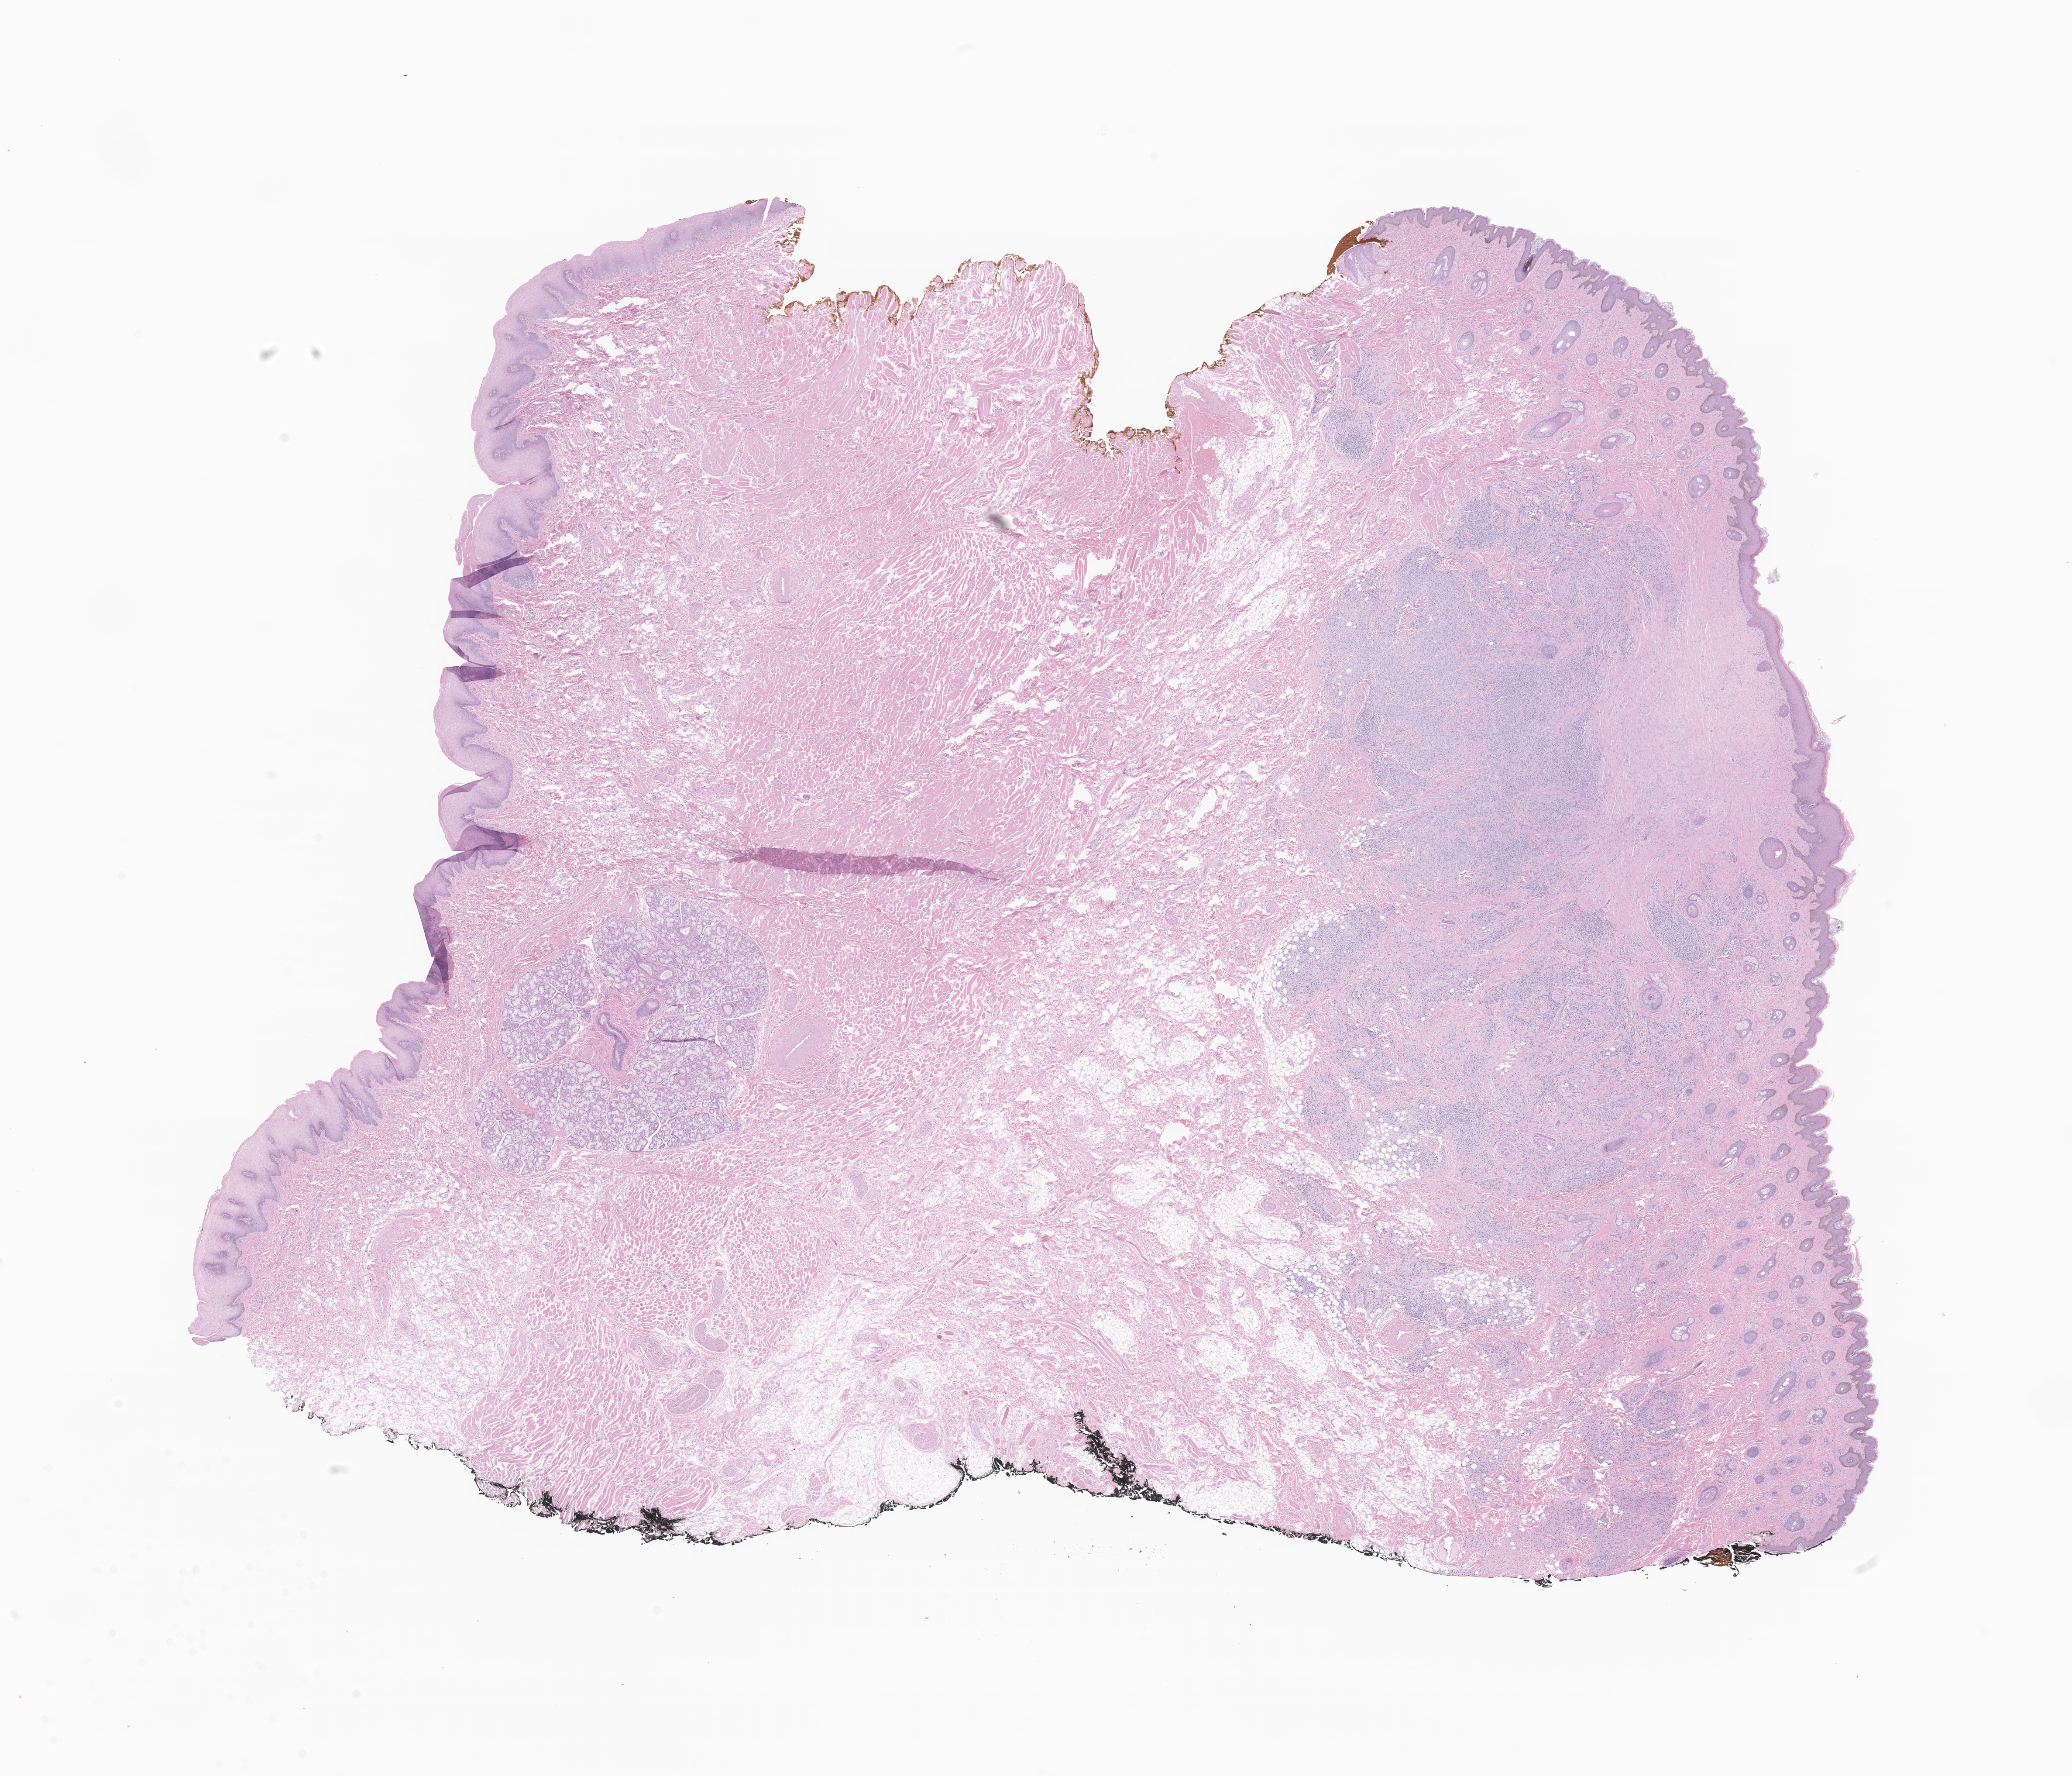
Hematoxylin and eosin (H&E) whole-slide image of tumor tissue from the lip, a low-resolution overview of the entire scanned area, about 20.0 x 17.1 mm, formalin-fixed paraffin-embedded section. Patient: female, age 82 months.
Diagnosis (ICD-O-3 morphology term): Rhabdomyosarcoma, NOS.